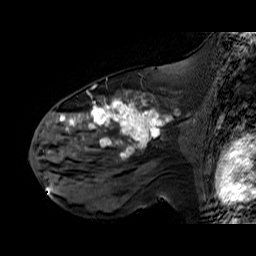
Breast MRI (dynamic contrast-enhanced), one sagittal slice. Position 37 of 60 along the scan axis. Dynamic contrast-enhanced series, time point 2 of 6 at this slice position (early post-contrast). 1.5 T. TE 6.3 ms, TR 32.9 ms. 4 mm slice thickness. 256 × 256 image matrix, field of view 200 × 200 mm. Female patient. From the clinical record (not read from this slice): setting: breast cancer imaged before/during neoadjuvant chemotherapy; receptor status: HER2-positive.
Outlined on this slice (semi-automatically segmented with operator editing):
- analysis volume of interest (the breast-tissue region the enhancement analysis was run in; not a lesion): bounding box <48,92,195,174> (left, top, right, bottom; pixels)
- tumour enhancement mask (voxels above the 100 % enhancement threshold inside the analysis volume of interest): <59,93,166,157>